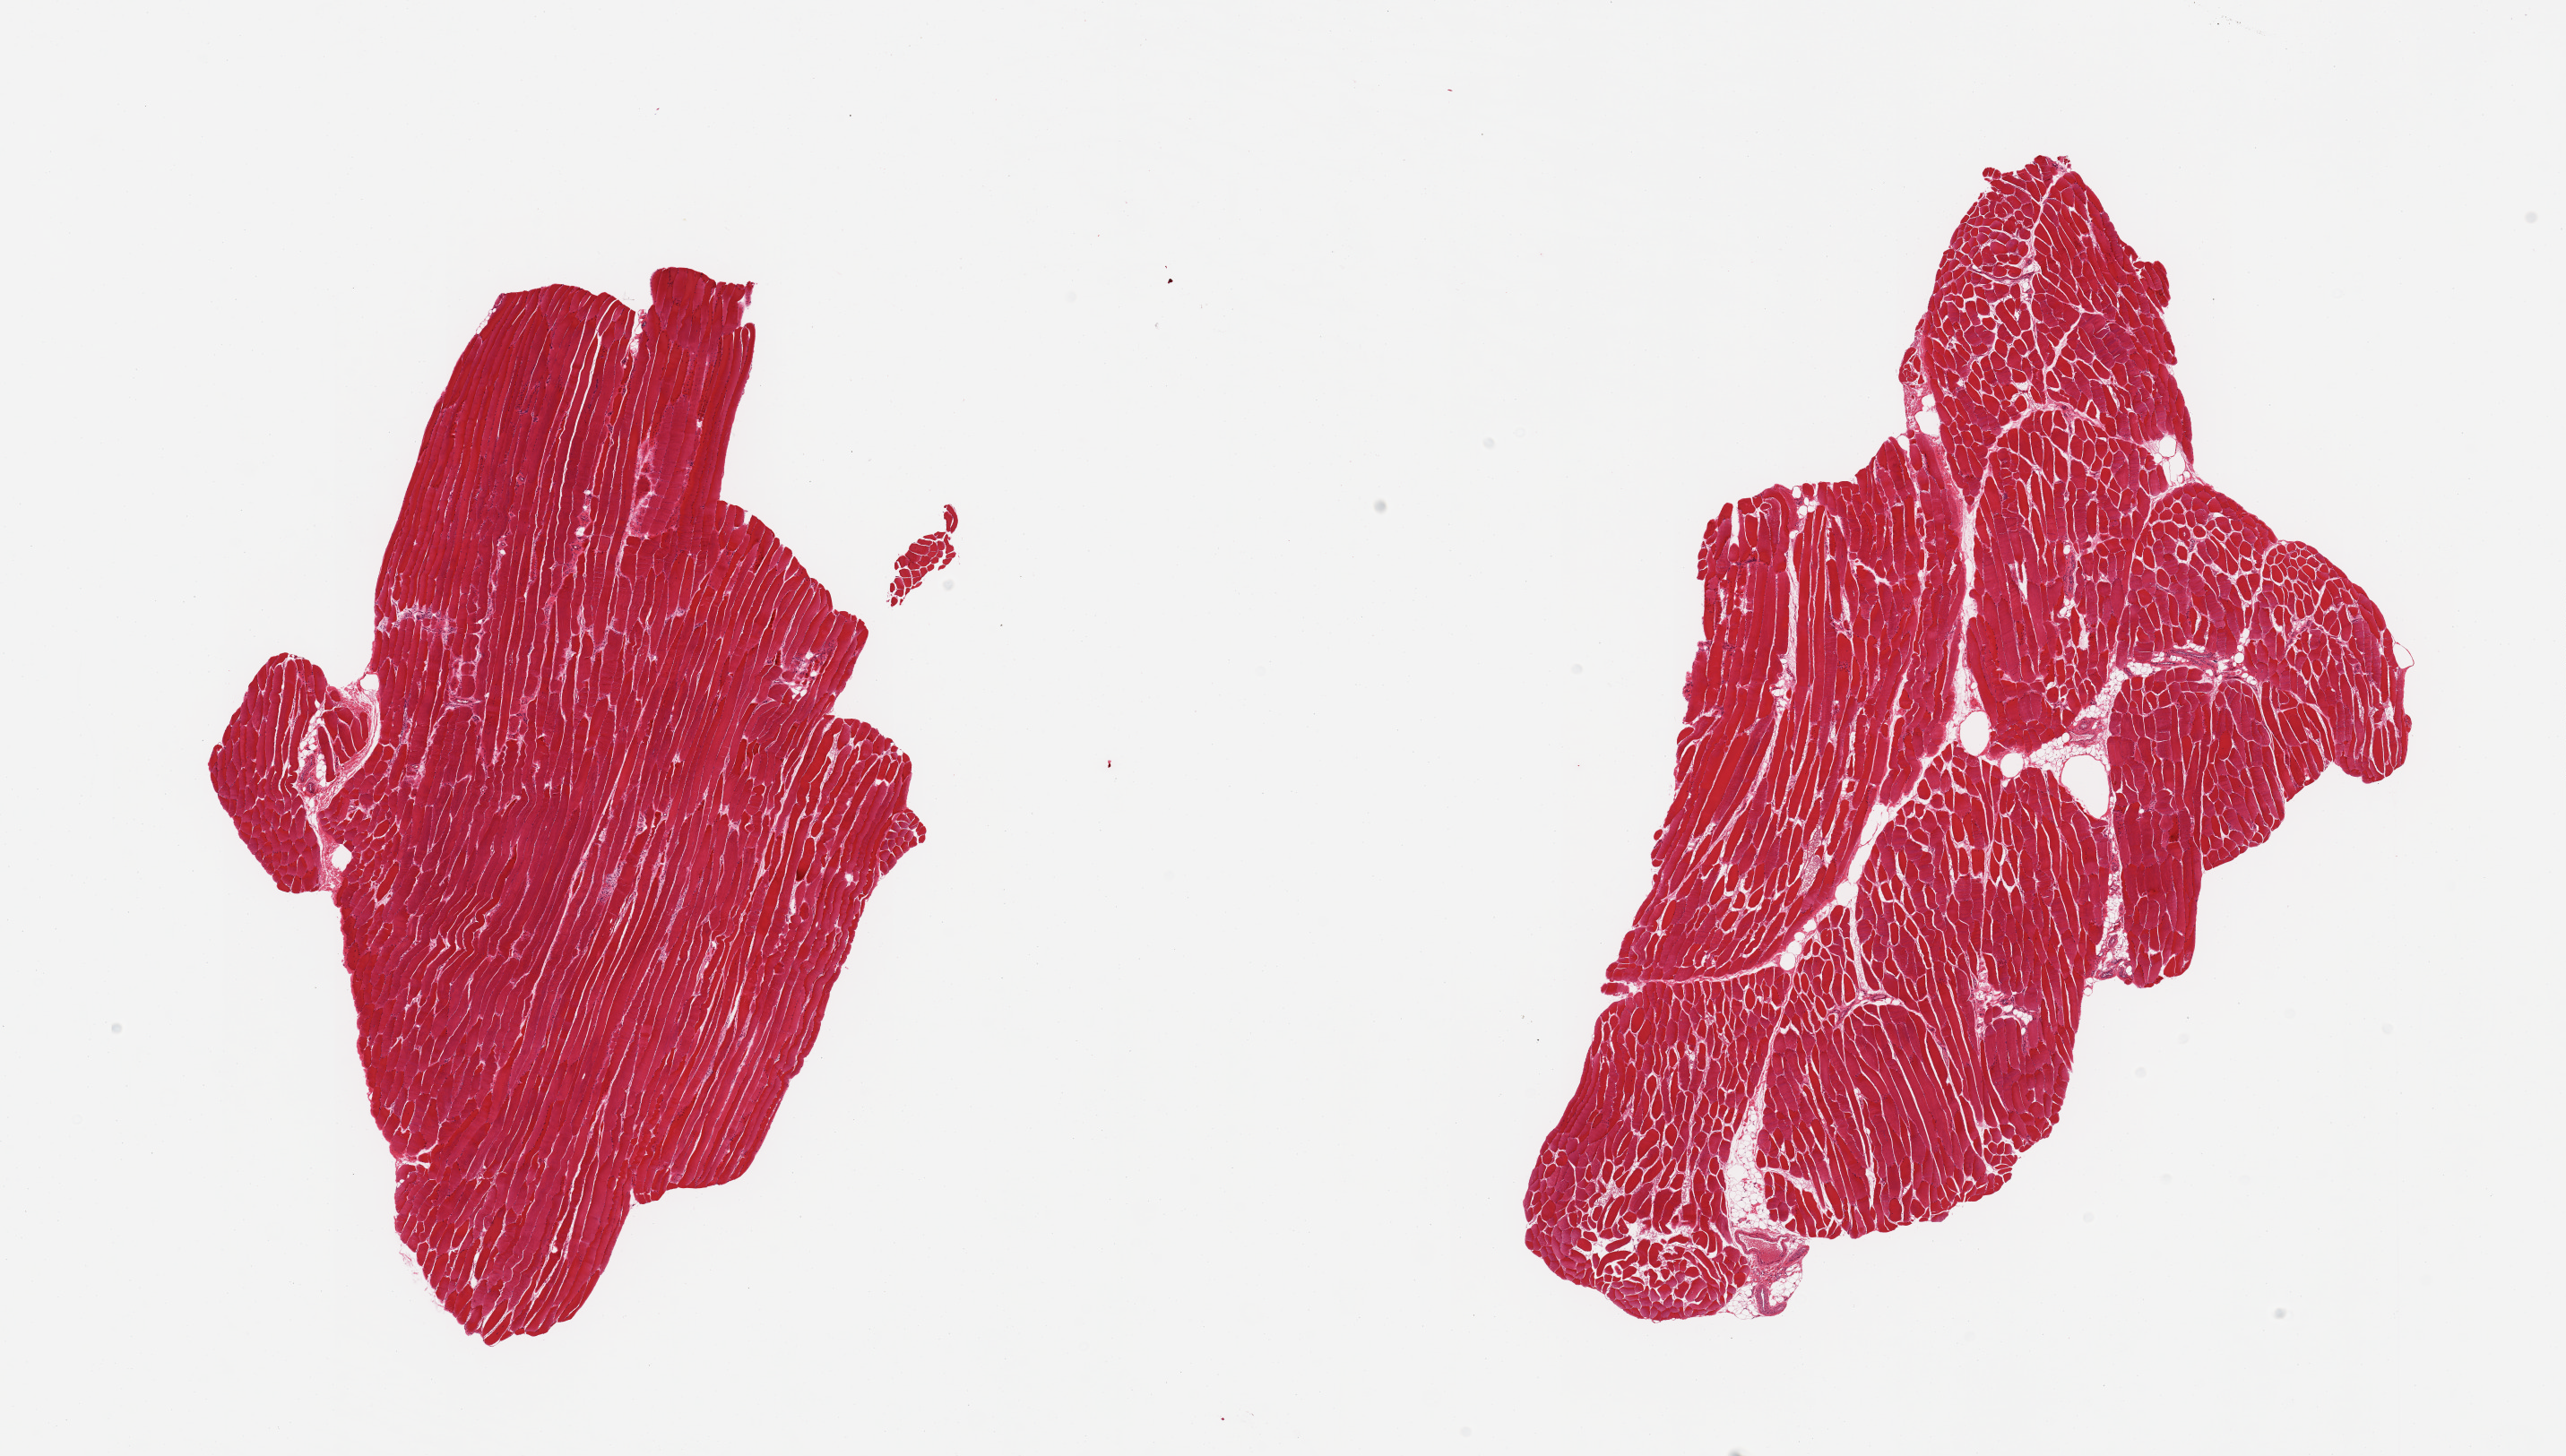
Whole-slide image, haematoxylin and eosin stain — shown as a low-resolution overview of the whole scanned area (about 22.6 x 12.9 mm, acquisition: 20x scan); PAXgene-fixed paraffin-embedded (PFPE) section; section of skeletal muscle (target tissue); tissue donor sample. Donor sex: male.
- pathologist's review note for this sample: 2 pieces, trace interstitial fat